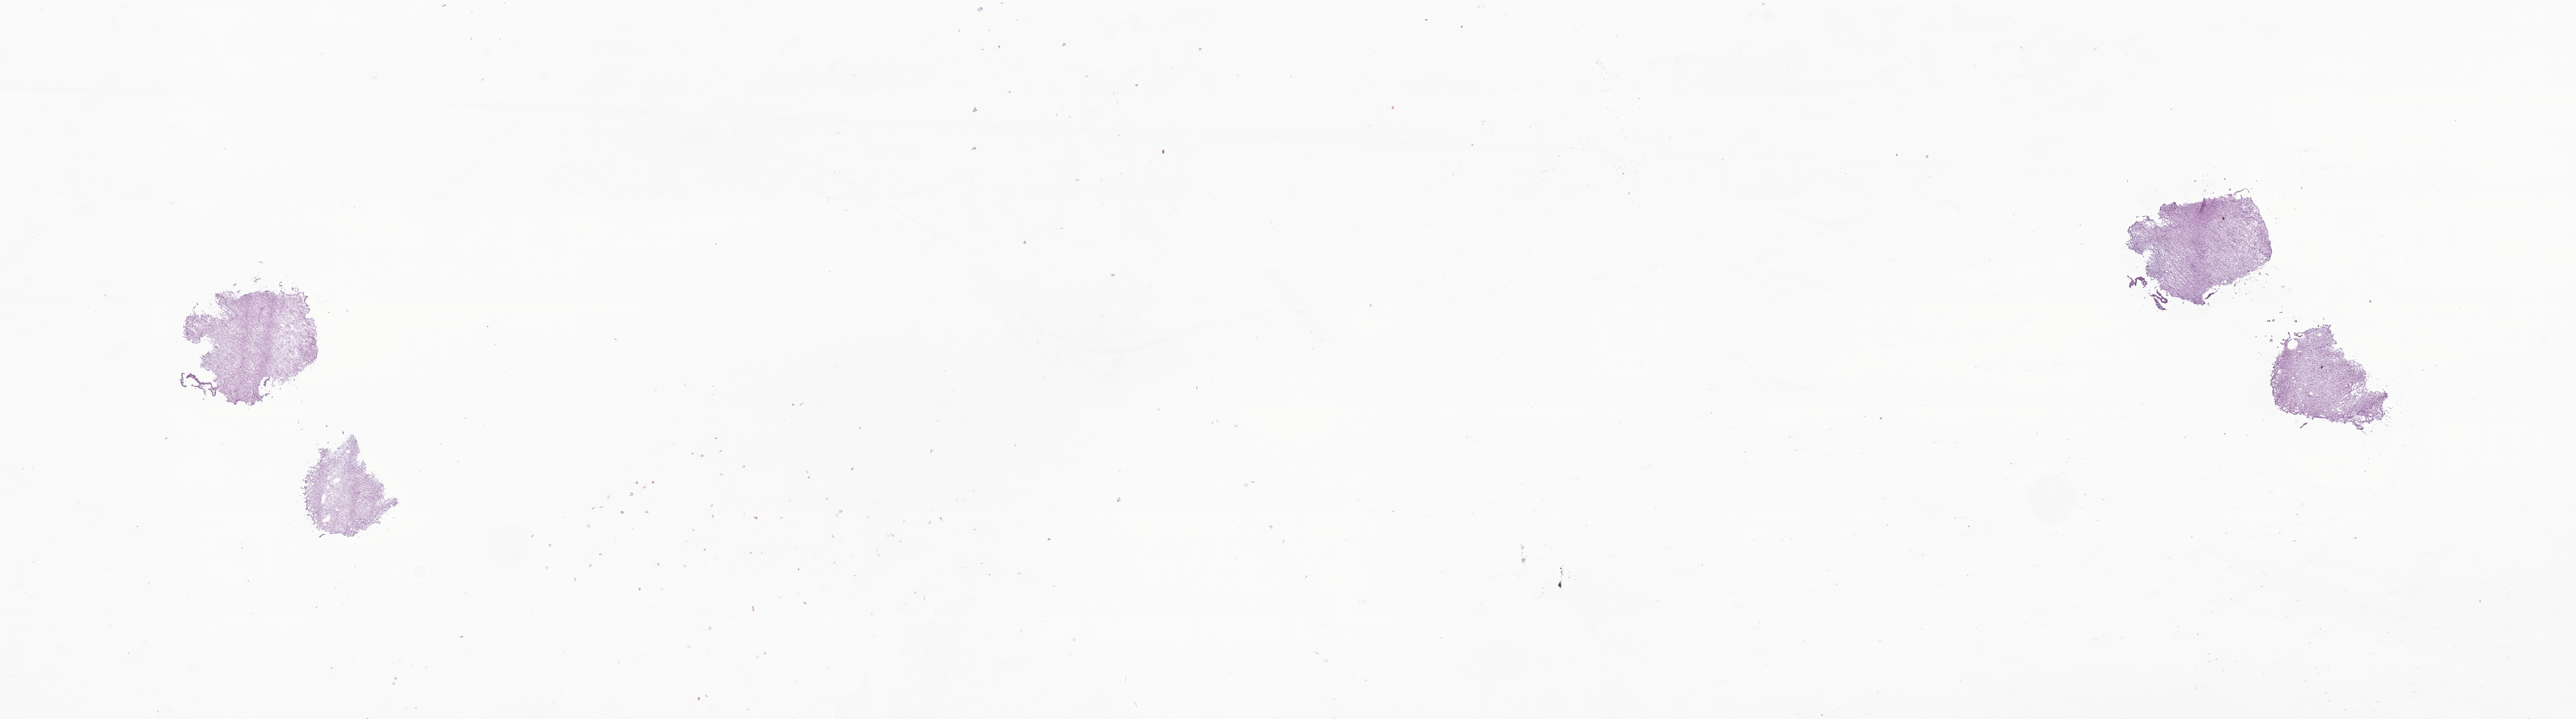
Whole-slide image, hematoxylin and eosin (H&E) stain of tumor tissue from the cerebellum, shown as a low-resolution overview of the whole scanned area (about 26.3 x 7.3 mm), frozen section (OCT-embedded). Patient: male, age 180 months.
• recorded diagnosis: Pilocytic astrocytoma